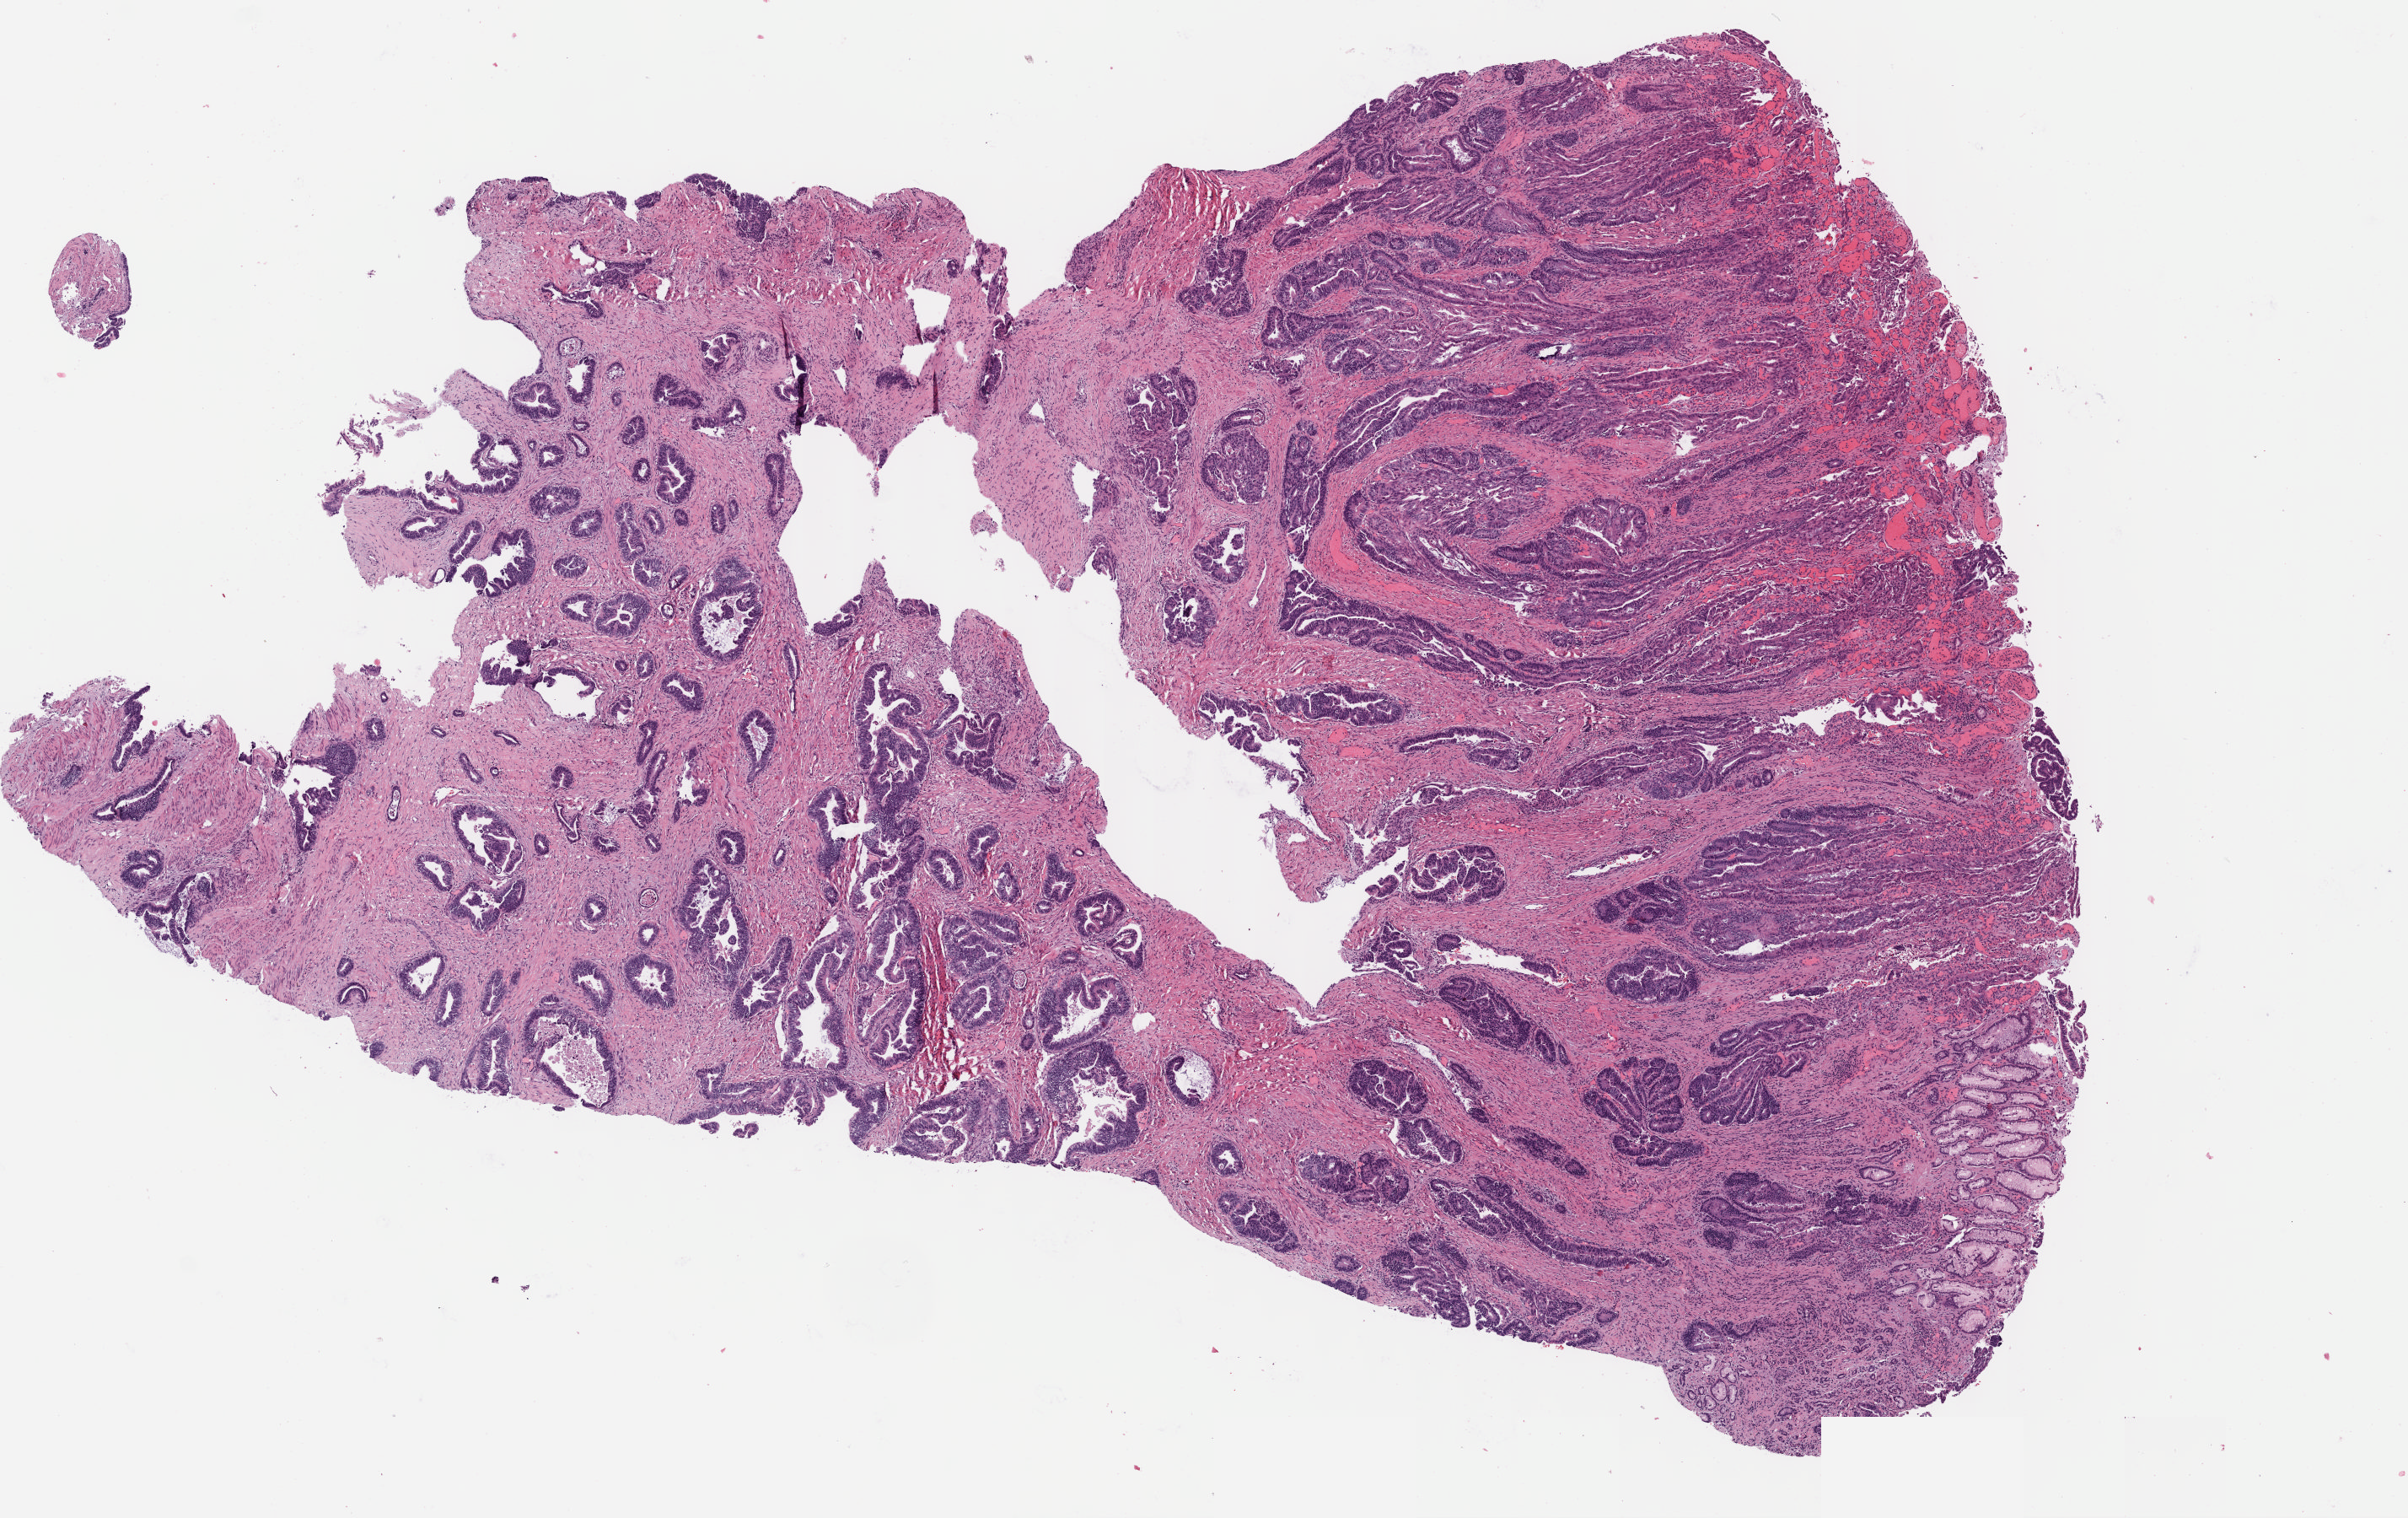
Digitized H&E-stained tissue section (whole slide), low-resolution overview of the scanned area, about 11.2 x 7.1 mm, FFPE section, primary tumour sample from the esophagus. Male patient; age at initial diagnosis 76 years. Histologic grade: G2 (moderately differentiated).
Pathologic diagnosis: Adenocarcinoma, NOS (lower third of esophagus). AJCC pathologic stage: IIIA (7th edition).